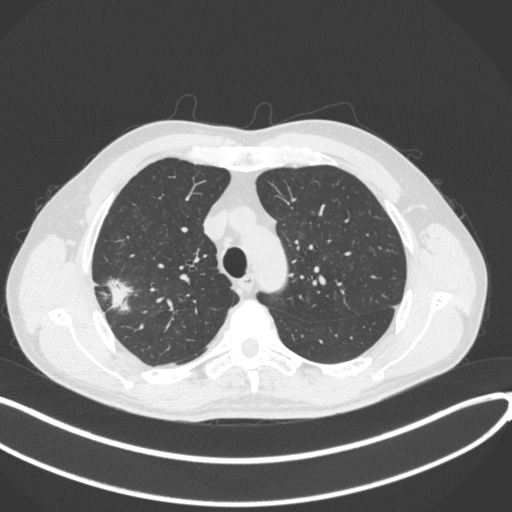
Chest CT, one axial slice; position 316 of 381 along the scan axis; reconstruction kernel B31f; 120 kVp; lung window (W 1500 / L -600 HU); 512 × 512 image matrix, field of view 400 × 400 mm. Male patient, age 62 years. From the clinical record (not read from this slice): clinical TNM (as recorded): T1c N0 M0.
Outlined on this slice (bounding box drawn by a radiologist):
- lung tumour (recorded histology: adenocarcinoma): bounding box [x1, y1, x2, y2] px = [102, 275, 137, 316]